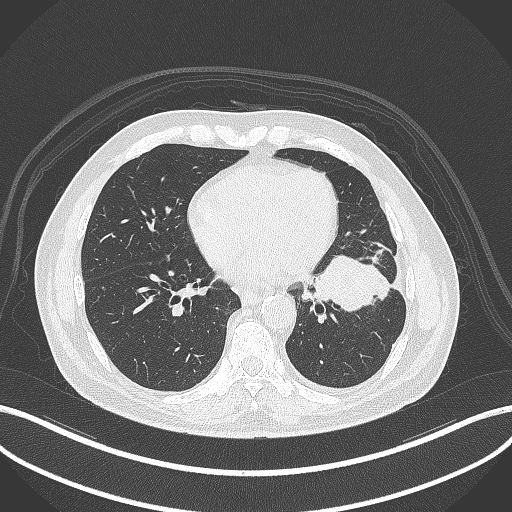
Chest CT, one axial slice. Position 141 of 230 along the scan axis. 120 kVp. Lung window (W 1500 / L -600 HU). 1 mm slice thickness. 512 × 512 image matrix, field of view 400 × 400 mm. Patient: male, 68 years. Case-level facts recorded for this patient, not image findings: clinical TNM (as recorded): T2b N0 M0.
Annotated regions visible in this slice (bounding box drawn by a radiologist):
- lung tumour (recorded histology: squamous cell carcinoma): box from (x=310, y=250) to (x=393, y=315) px